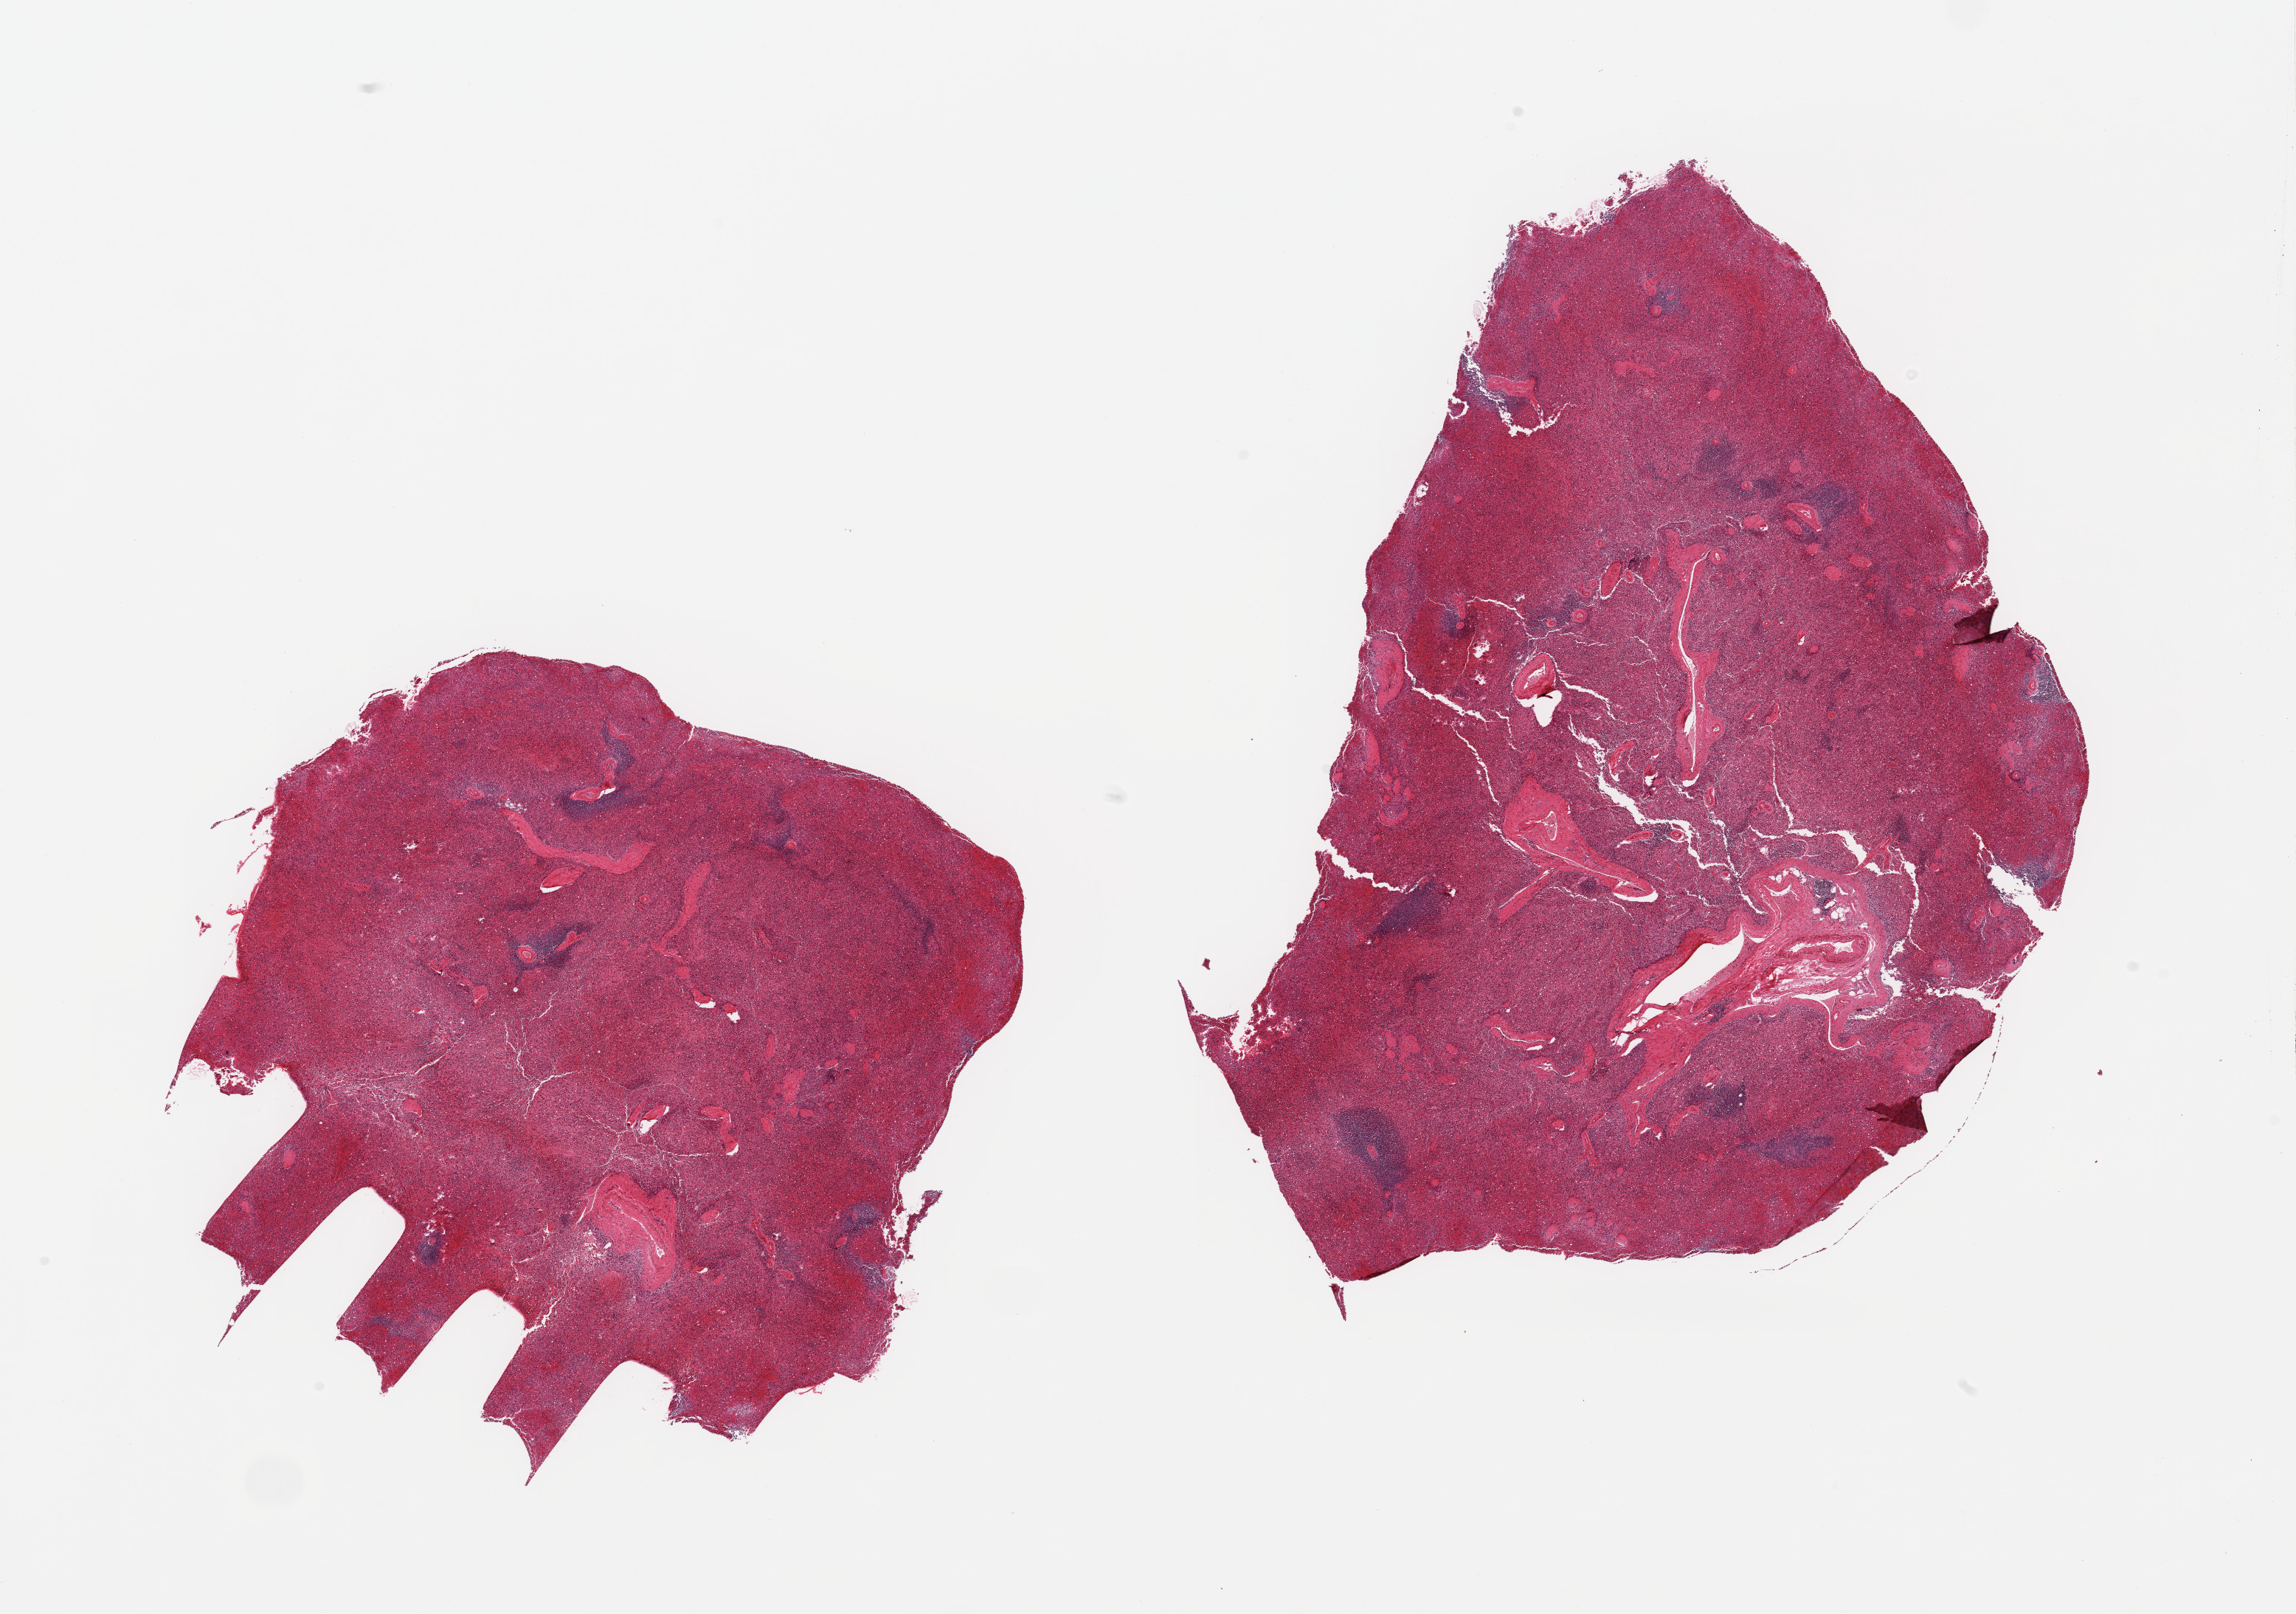
Digitized hematoxylin and eosin (H&E)-stained section, brightfield, shown as a low-resolution overview of the whole scanned area (about 24.6 x 17.3 mm, from a 20x scan). PAXgene-fixed paraffin-embedded (PFPE) section. Target tissue: spleen. Donor tissue sample. Donor: female.
- reviewer comment on this tissue sample: 2 pieces; moderately congested